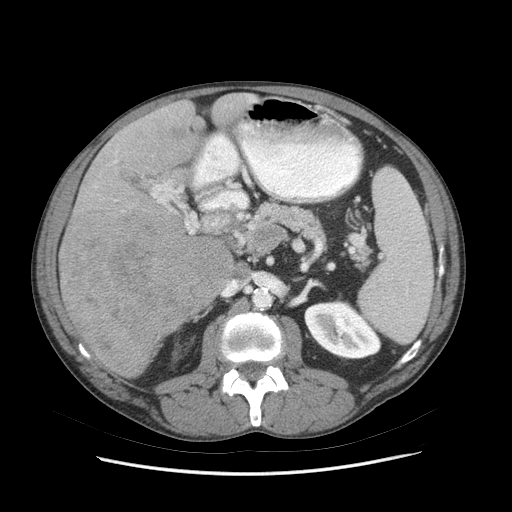
Contrast-enhanced abdominal CT (liver protocol), one axial slice; slice 34 of 89 in the series (ordered by position); soft-tissue window (W 400 / L 40 HU); 2.5 mm slice thickness; 512 × 512 image matrix, field of view 380 × 380 mm. From the clinical record (not read from this slice): diagnosis: hepatocellular carcinoma (patient treated with transarterial chemoembolisation; whether this scan precedes or follows treatment is not stated here); TNM stage (as recorded): Stage-IIIB; Child-Pugh class: A; tumour differentiation: moderately differentiated; tumour nodularity: multinodular.
Structures marked on this image (semi-automatically segmented with operator editing):
- liver parenchyma outside the tumour (the mass and vessels are separate outlines, so this box may not span the whole liver): bounding box <58,92,258,378> (left, top, right, bottom; pixels)
- mass: <60,206,235,377>
- liver vessels: <115,96,255,163>